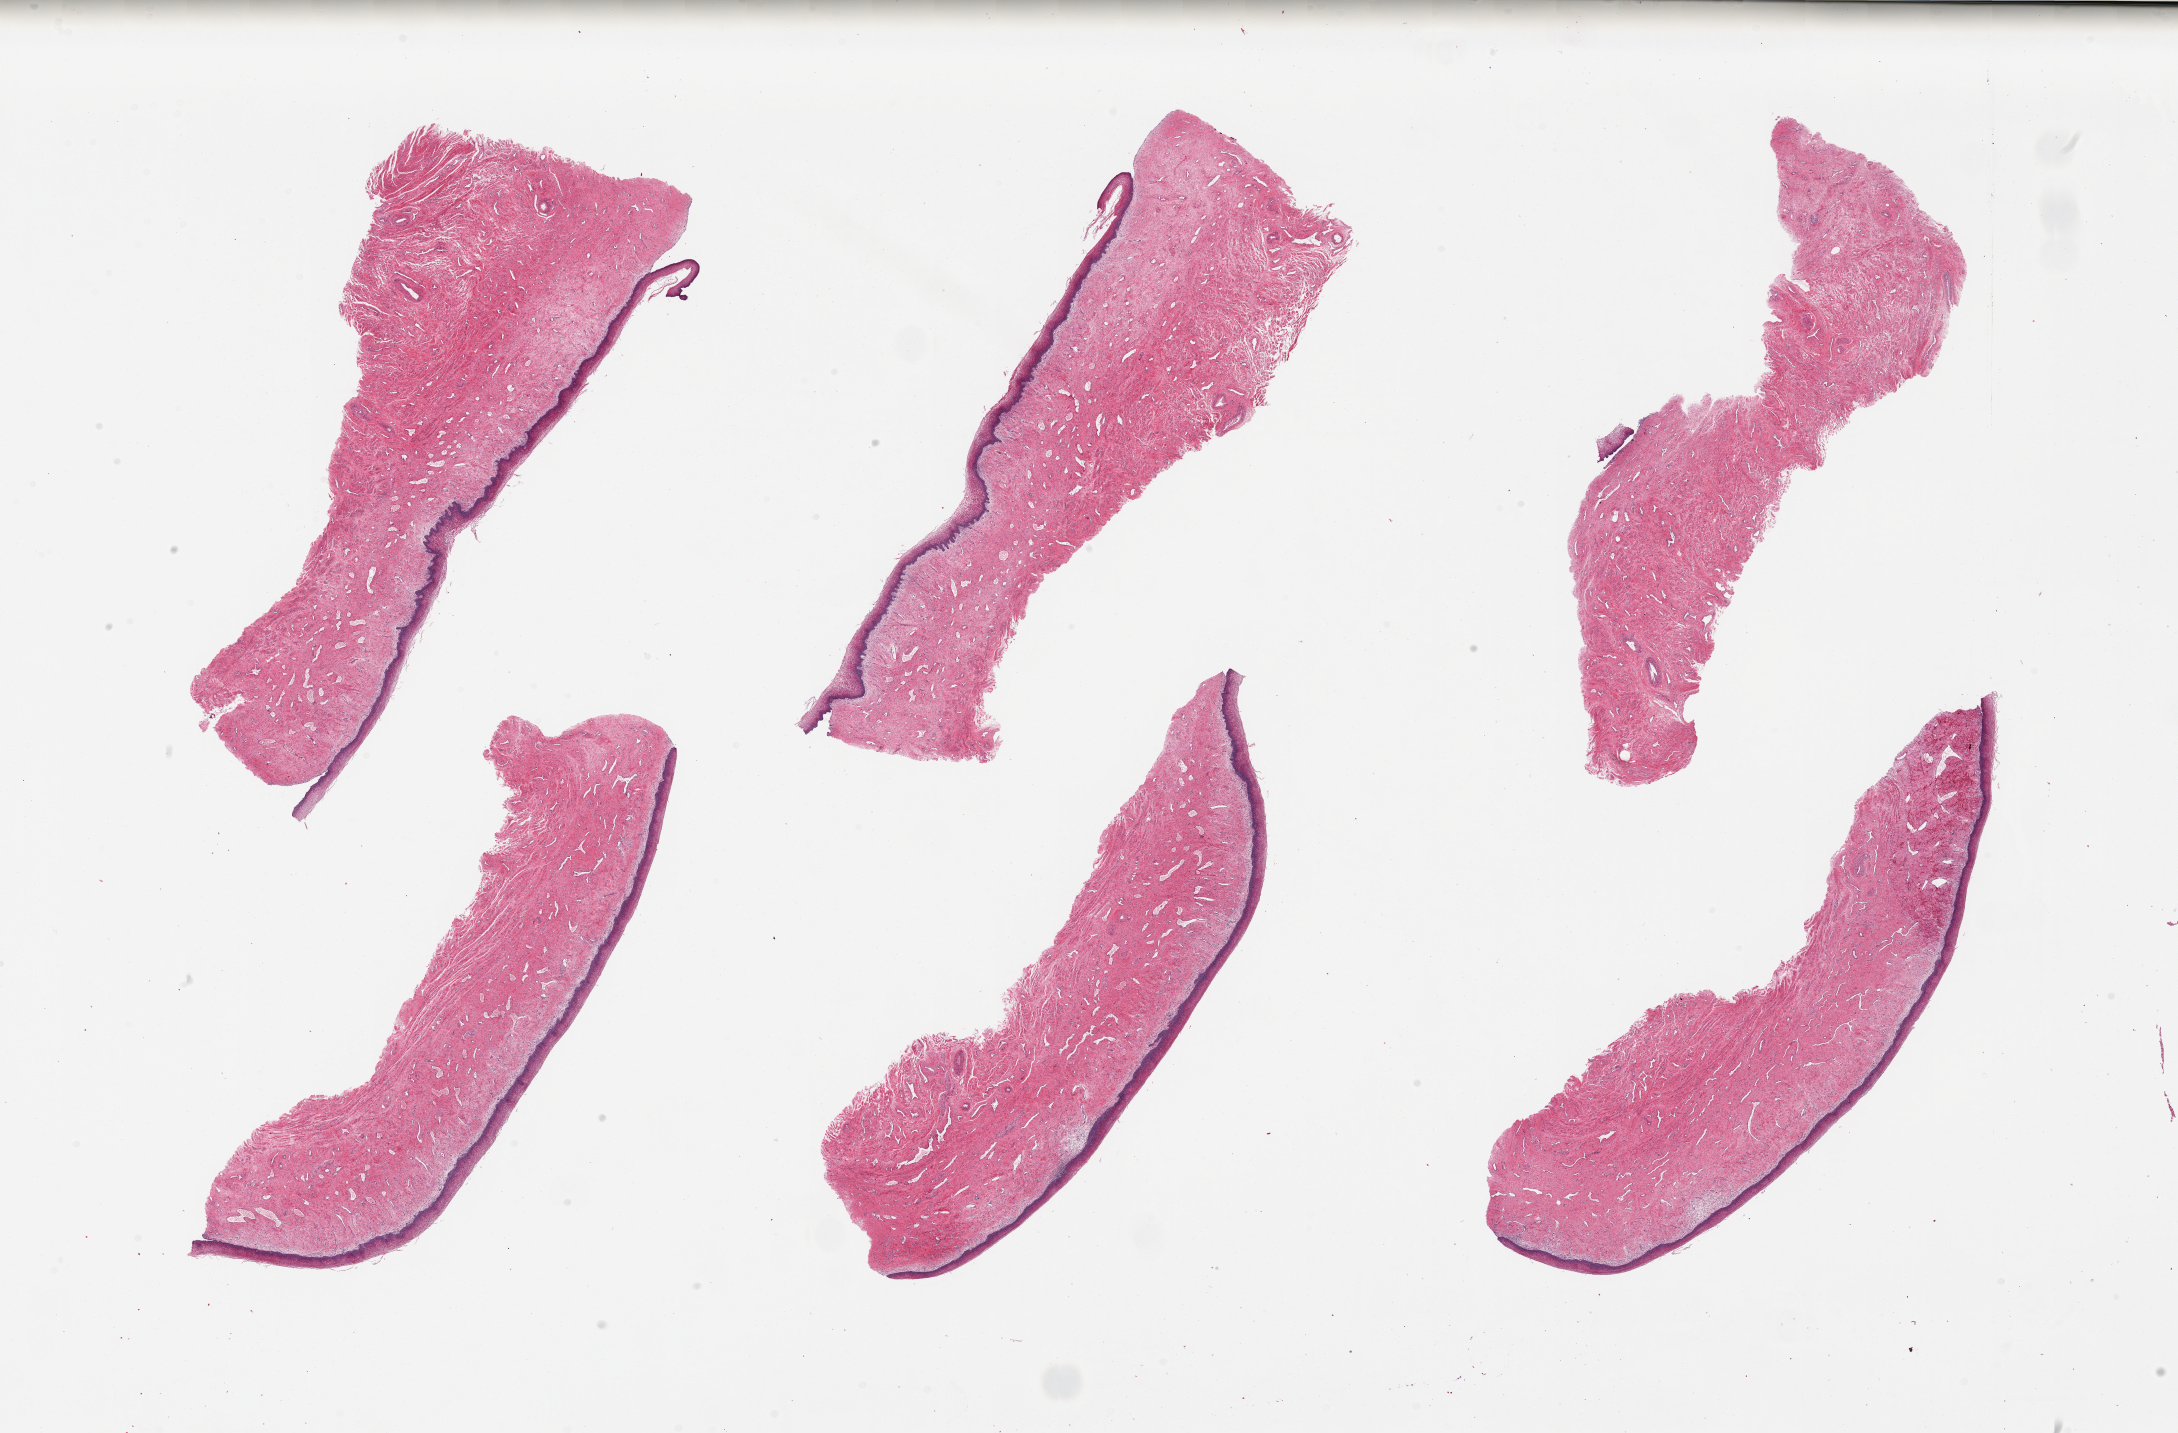
Whole-slide image, hematoxylin and eosin (H&E) stain, brightfield, shown as a low-resolution overview of the whole scanned area (about 34.5 x 22.7 mm, slide scanned at 20x); PAXgene-fixed, paraffin-embedded tissue; section of vagina (target tissue); tissue donor sample. Female donor.
Review note (as recorded): 6 pieces, up to 12x5mm. 1 with minimal epithelium.